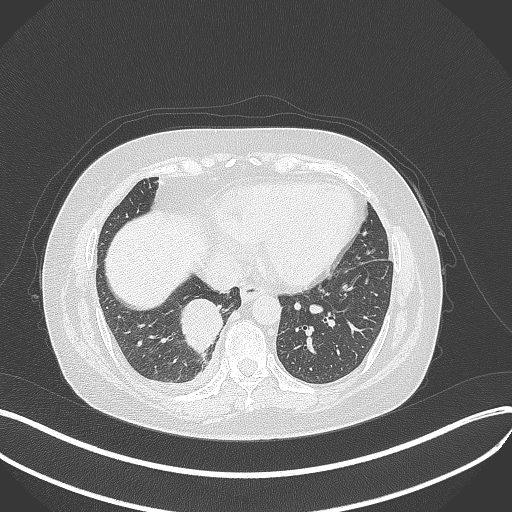
Chest CT, one axial slice. Position 113 of 381 along the scan axis. Lung window (W 1500 / L -600 HU). 512 × 512 image matrix, field of view 400 × 400 mm. Patient: female, 56 years. From the clinical record (not read from this slice): clinical TNM (as recorded): T2b N1 M0; histopathological grade: G3.
Structures marked on this image (rectangle marked by the reading radiologist):
- lung tumour (recorded histology: small cell carcinoma): bounding box <179,297,227,361> (left, top, right, bottom; pixels)